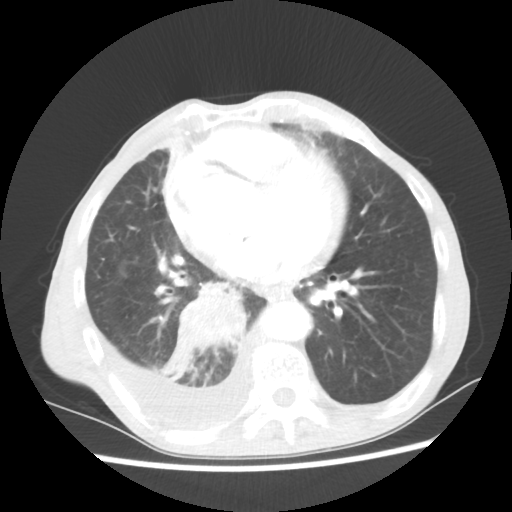
Chest CT, one axial slice. Reconstruction kernel STANDARD. Lung window (W 1500 / L -600 HU). 5 mm slice thickness. 512 × 512 image matrix, field of view 335 × 335 mm. Male patient, age 76 years. From the clinical record (not read from this slice): clinical TNM (as recorded): T3 N3 M1a; histopathological grade: G3.
Structures marked on this image (rectangle marked by the reading radiologist):
- lung tumour (recorded histology: squamous cell carcinoma): bounding box (x1, y1, x2, y2) in pixels: (153, 282, 251, 384)